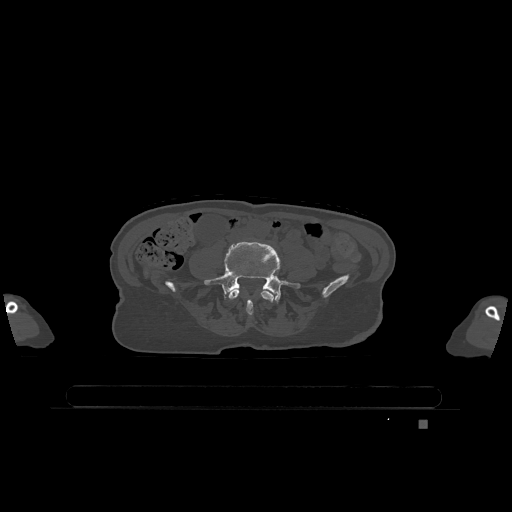
CT including the spine, one axial slice. Position 259 of 1317 along the scan axis. Bone window (W 1800 / L 400 HU). 512 × 512 image matrix. Female patient, age 74 years. Case-level facts recorded for this patient, not image findings: primary cancer: lung; vertebrae with lytic lesions (as recorded): T1, T4, T5, T6, L4, L5.
Annotated regions visible in this slice (semi-automatically segmented with operator editing):
- L4 vertebra: bounding box <228,289,274,318> (left, top, right, bottom; pixels)
- L5 vertebra: <204,242,300,304>